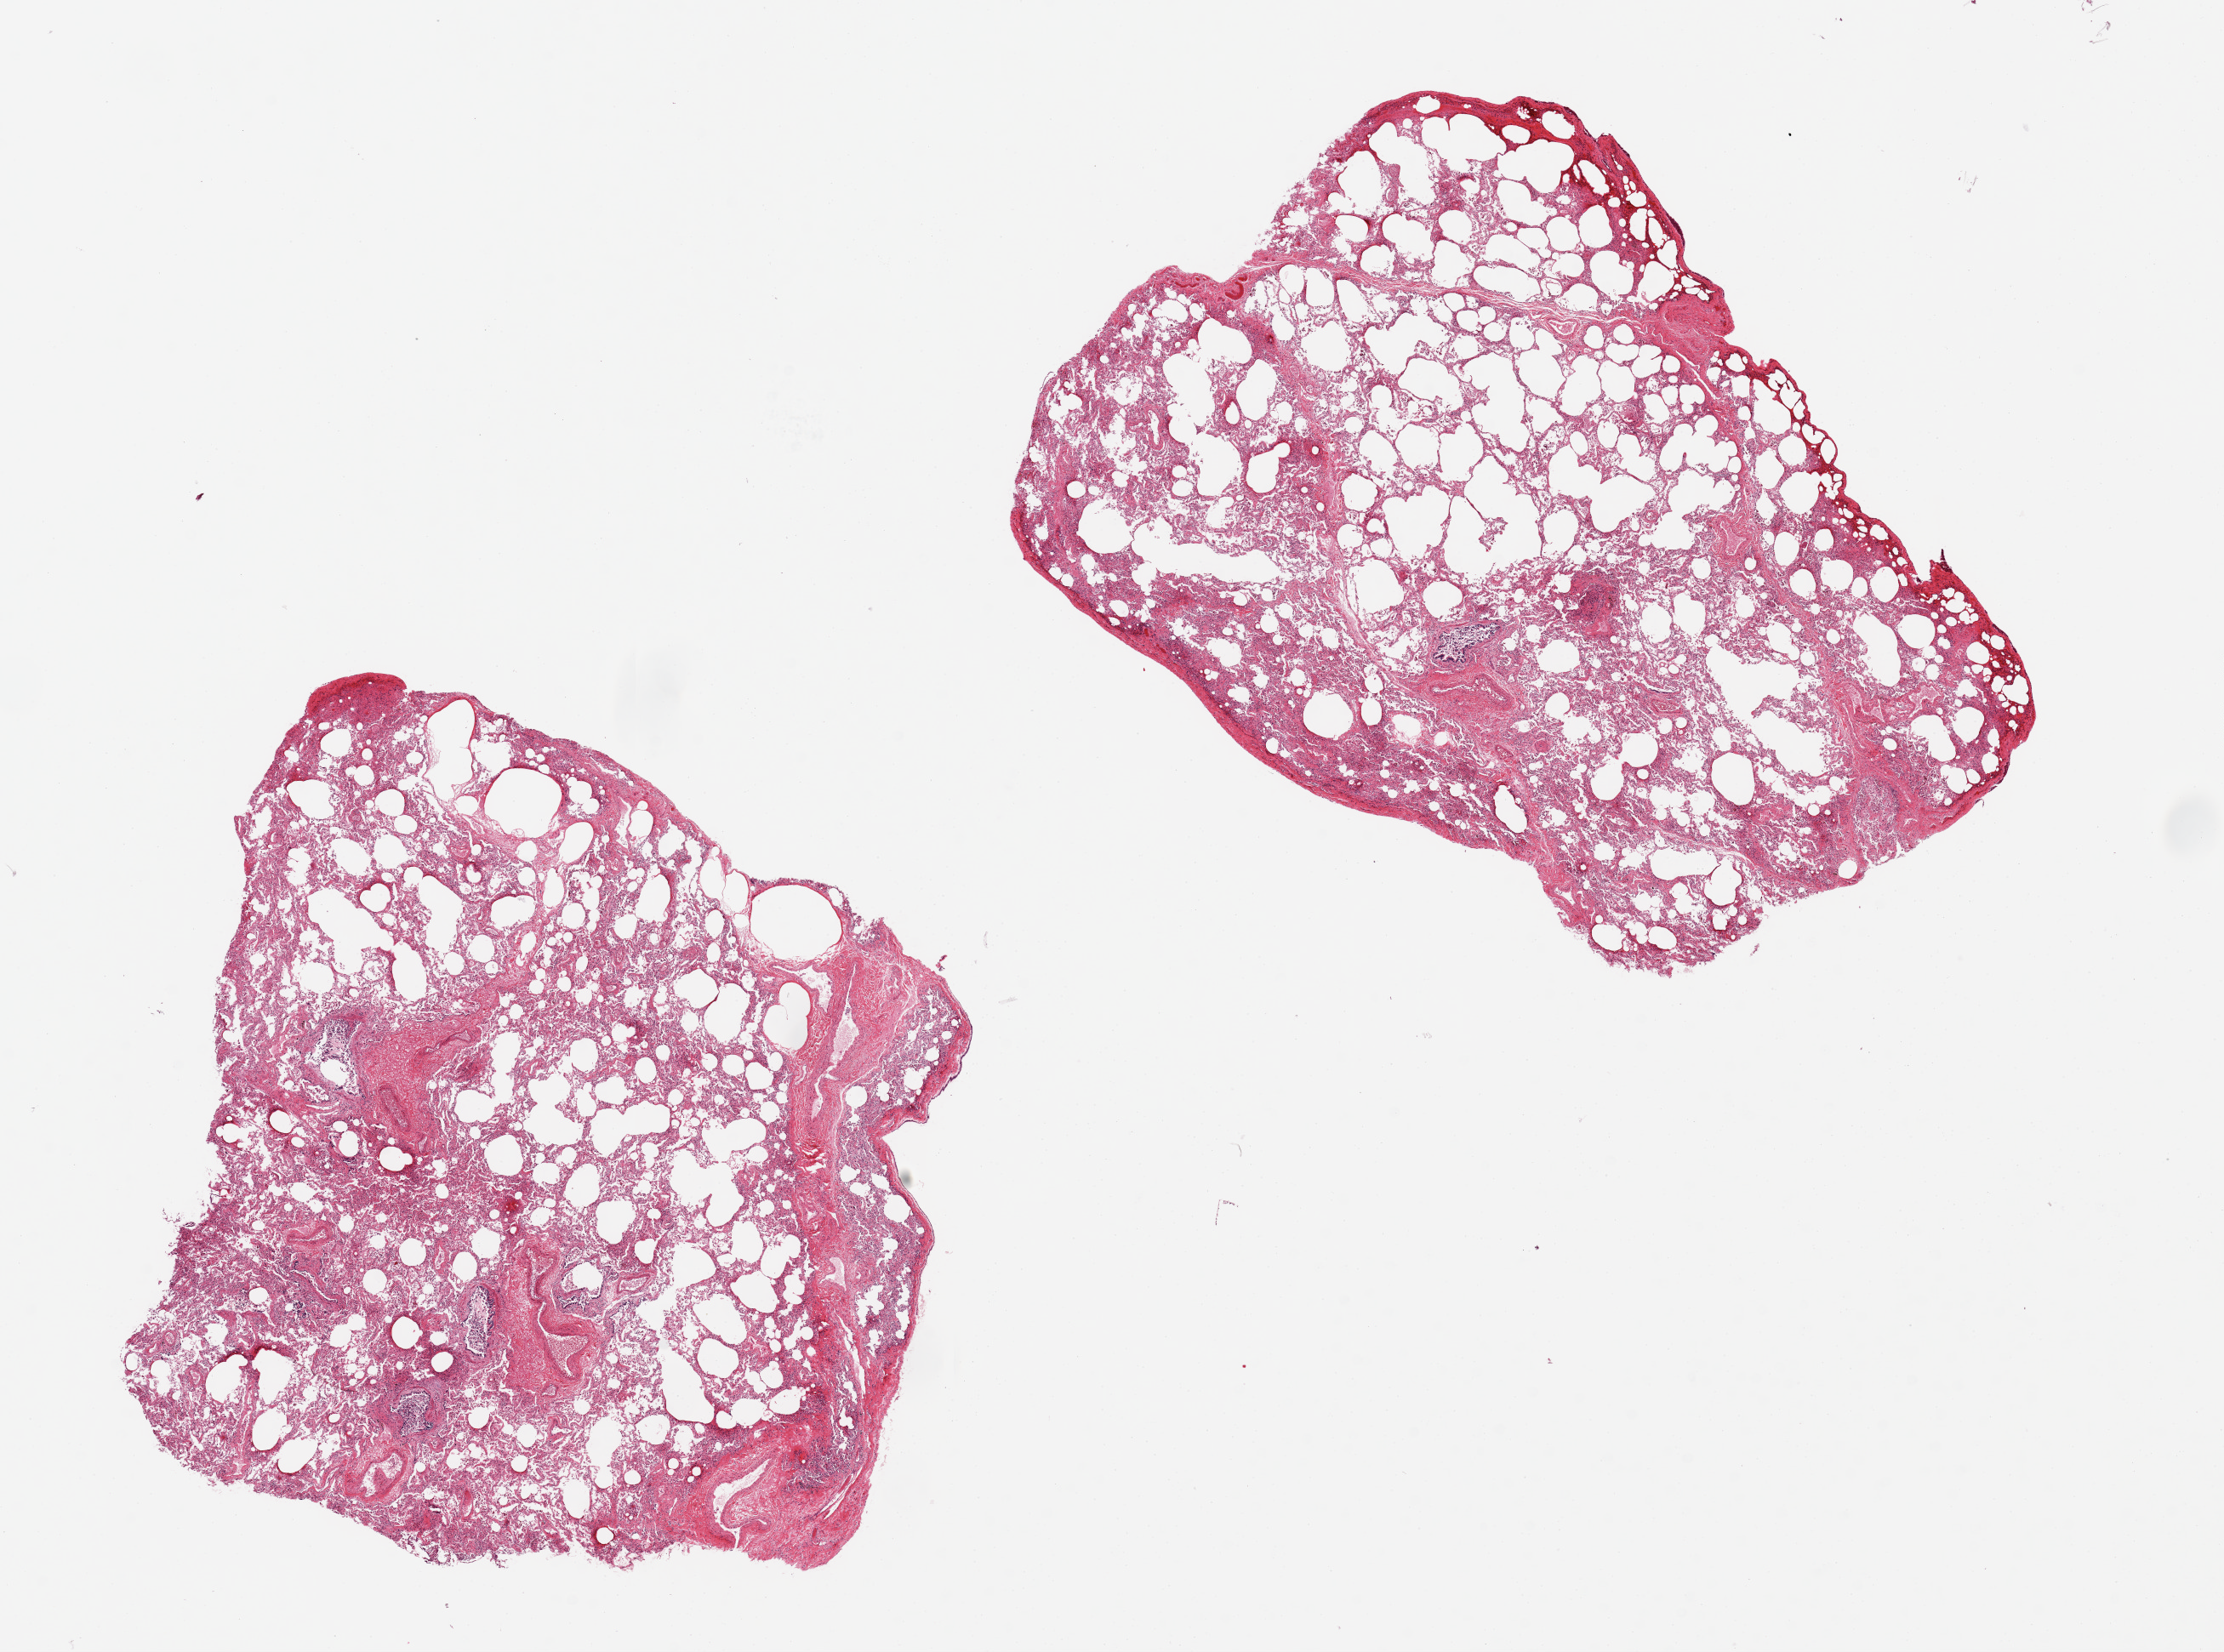
Whole-slide image, hematoxylin and eosin (H&E) stain — a low-resolution overview of the entire scanned area, about 20.7 x 15.4 mm (slide scanned at 20x); PAXgene-fixed, paraffin-embedded tissue; section of lung (target tissue); tissue donor sample. Male donor.
Reviewer comment on this tissue sample: 2 pieces, moderate congestion, moderately autolyzed.